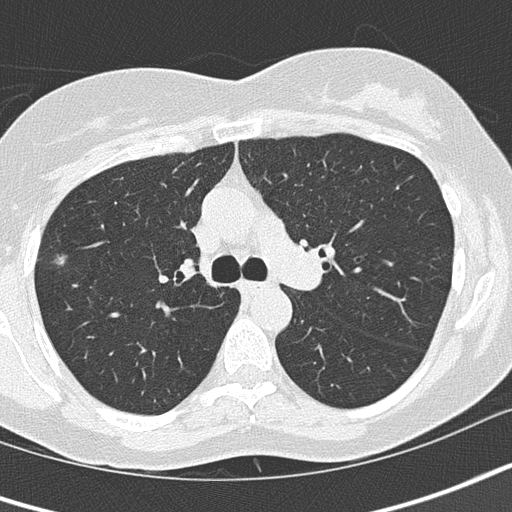
Chest CT (low-dose screening protocol), one axial image; baseline annual screen; lung window (W 1500 / L -600 HU); 2 mm slice thickness. Female participant, aged 64 years at enrolment.
Expert-annotated lung lesion, bounding box <33,236,83,284> (left, top, right, bottom; pixels). The screening reader recorded 4 non-calcified nodules or masses ≥4 mm on this exam (right upper lobe, left upper lobe, left upper lobe, left lower lobe); which of them this box marks is not recorded. Official screen result: positive, change unspecified: nodule(s) >= 4 mm or enlarging nodule(s), mass(es), or other non-specific abnormalities suspicious for lung cancer. Participant outcome: lung cancer diagnosed 447 days after this screen (after the second annual screen) — bronchiolo-alveolar adenocarcinoma, NOS, right upper lobe, well differentiated (G1), stage IA (AJCC 6th edition), 10 mm at pathology.